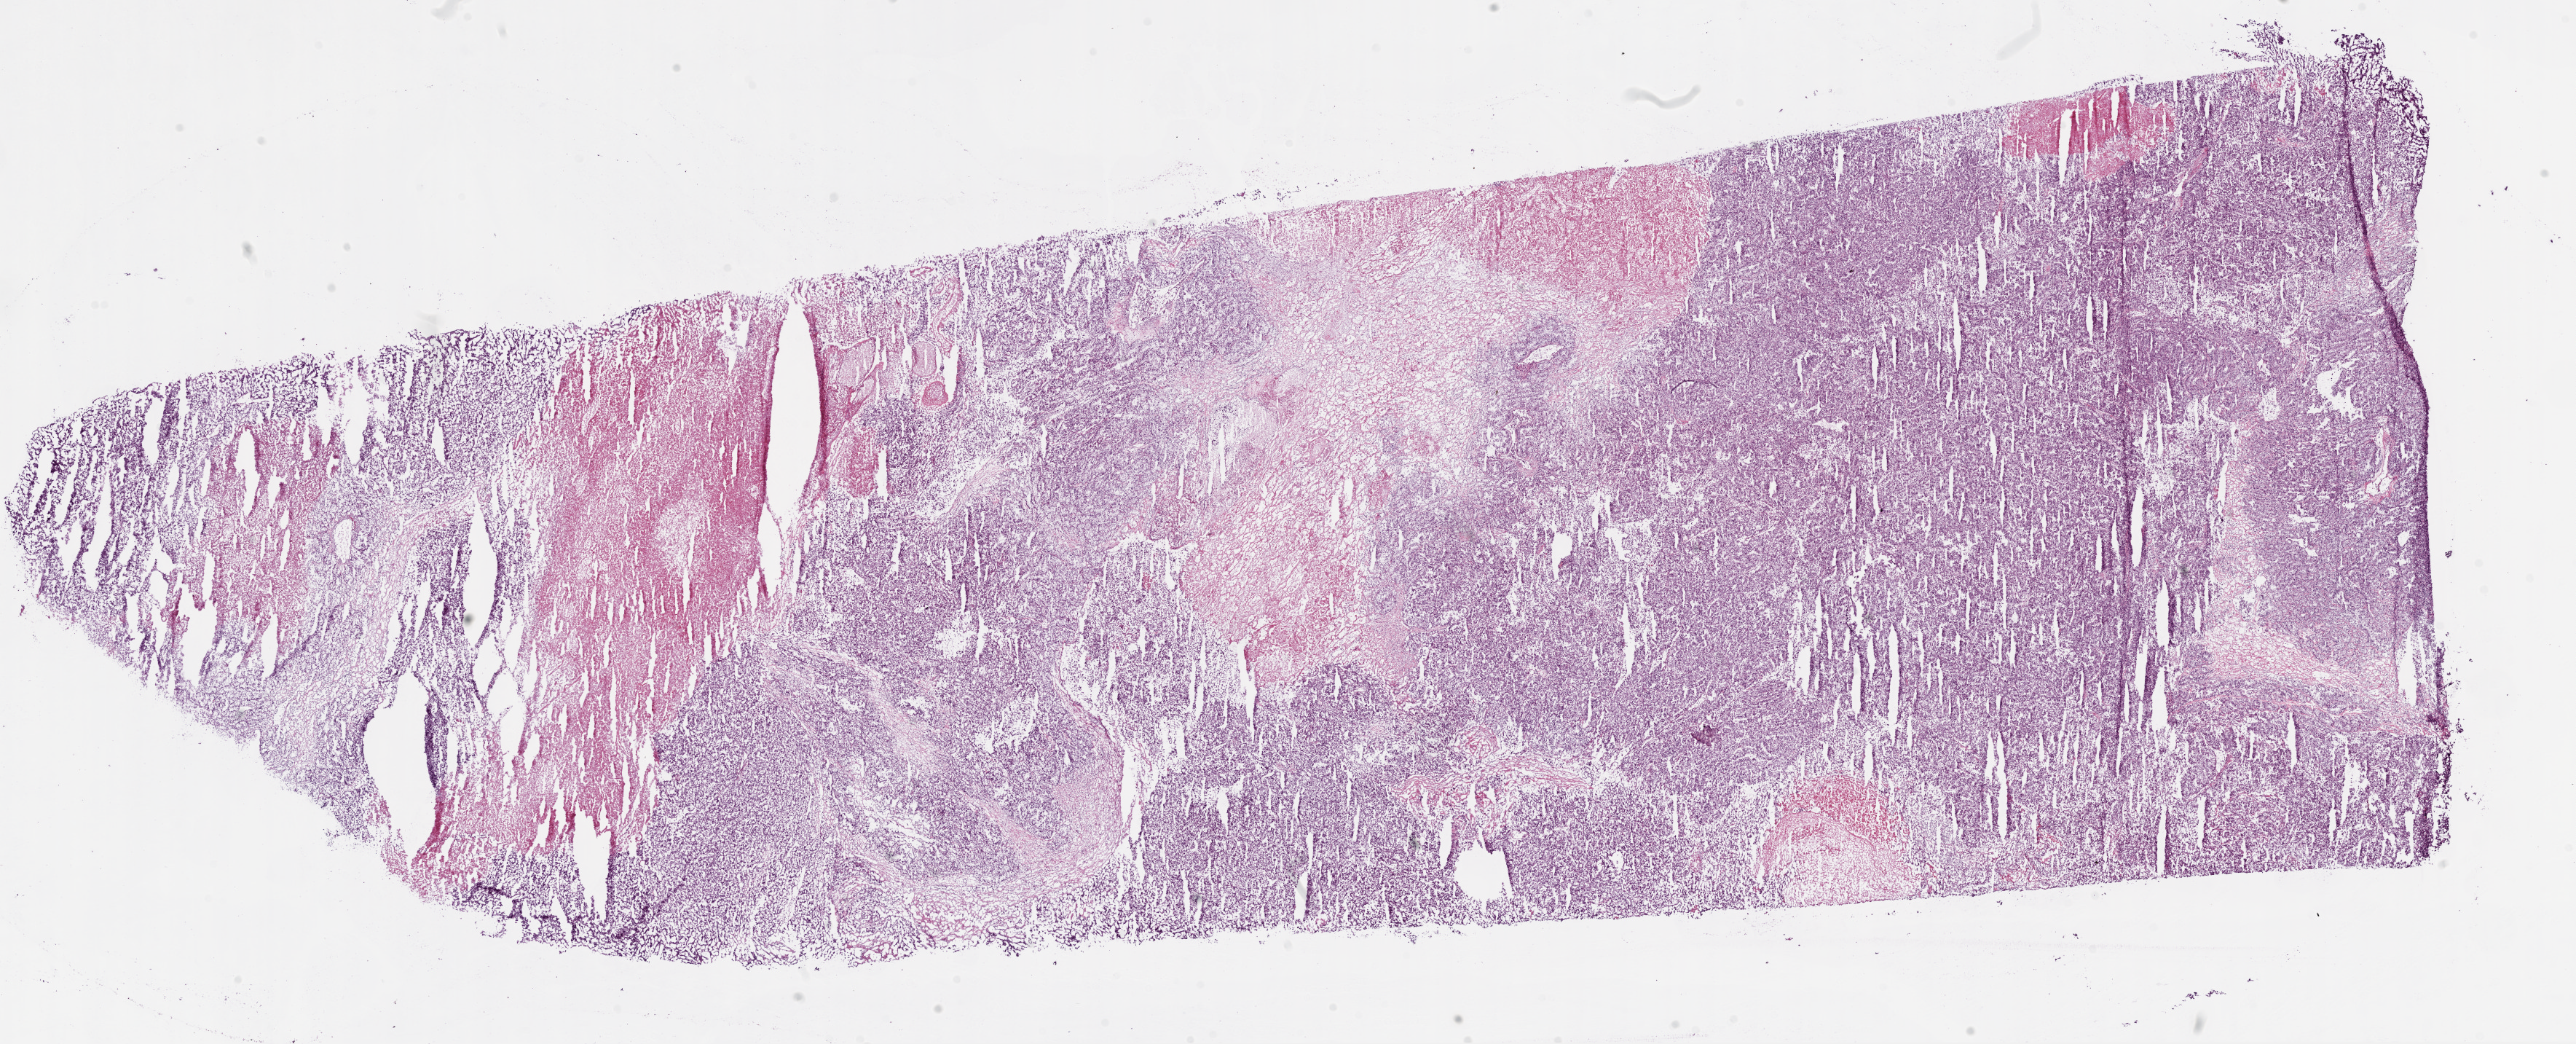
H&E whole-slide image, low-resolution overview of the scanned area, about 28.5 x 11.6 mm (slide scanned at 20x); frozen section; sample: primary tumour, kidney. Female patient; age at initial diagnosis 44 years. Histologic grade: G3 (poorly differentiated). Pathologist review of this section (percent, as recorded): tumour cells 88%, tumour nuclei 85%, normal cells 0%, stromal cells 12%, necrosis 12%.
AJCC pathologic stage: IV. Diagnosis: Clear cell adenocarcinoma, NOS.